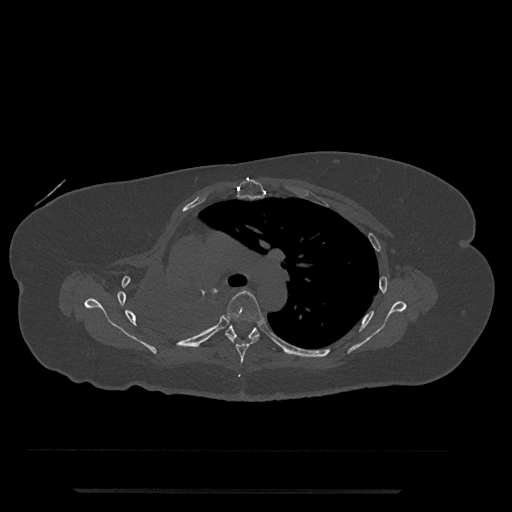
CT including the spine, one axial slice. Slice 523 of 797 in the series (ordered by position). 120 kVp. Bone window (W 1800 / L 400 HU). 0.5 mm slice thickness. 512 × 512 image matrix, field of view 440 × 440 mm. Female patient, age 51 years. From the clinical record (not read from this slice): primary cancer: neuro; vertebrae with lytic lesions (as recorded): T8.
Structures marked on this image (semi-automatic segmentation, software-assisted and operator-edited):
- T5 vertebra: bounding box <225,290,264,364> (left, top, right, bottom; pixels)
- T6 vertebra: <225,325,275,350>